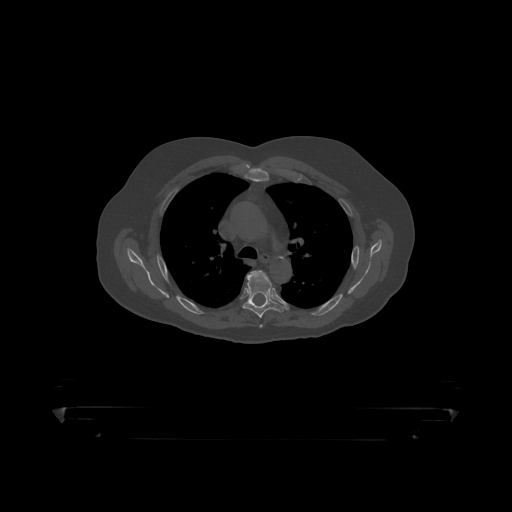
CT including the spine, one axial slice. Reconstruction kernel STANDARD. 120 kVp. Bone window (W 1800 / L 400 HU). 1.25 mm slice thickness. 512 × 512 image matrix. Male patient, age 60 years. Case-level facts recorded for this patient, not image findings: primary cancer: prostate.
Annotated regions visible in this slice (semi-automatically segmented with operator editing):
- T5 vertebra: bounding box (x1, y1, x2, y2) in pixels: (244, 271, 285, 319)